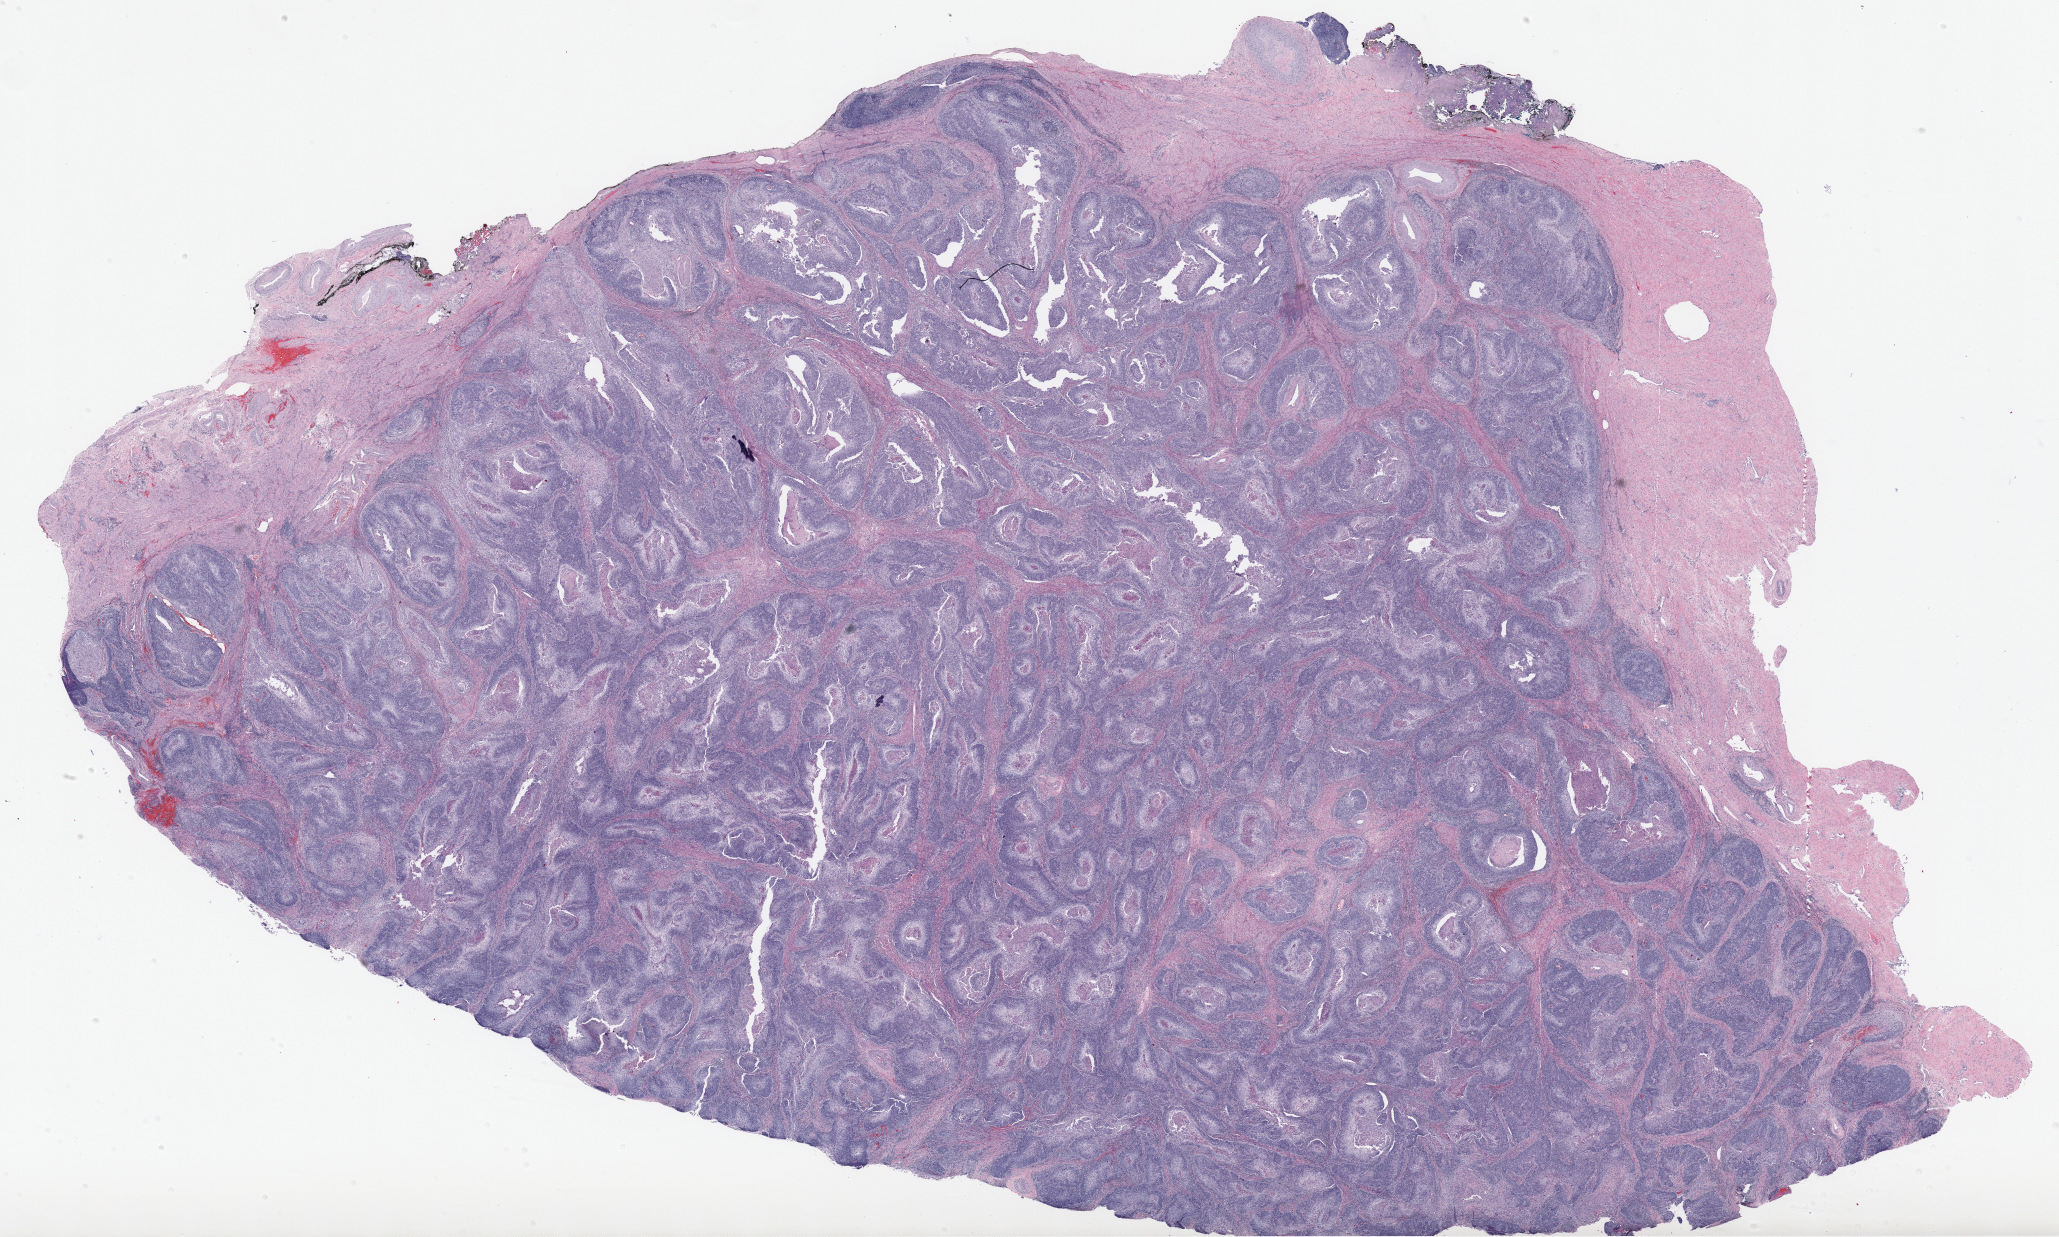
H&E-stained whole-slide image, whole scanned area (about 32.8 x 19.7 mm, from a 20x scan) shown as a low-resolution overview, formalin-fixed paraffin-embedded (FFPE) diagnostic section, sample: primary tumour, cervix. Patient: female, age at initial diagnosis 60 years. Histologic grade: G2 (moderately differentiated).
* diagnosis: Squamous cell carcinoma, NOS
* FIGO stage: IB1
* lymph nodes positive (case pathology): 0 of 15 examined